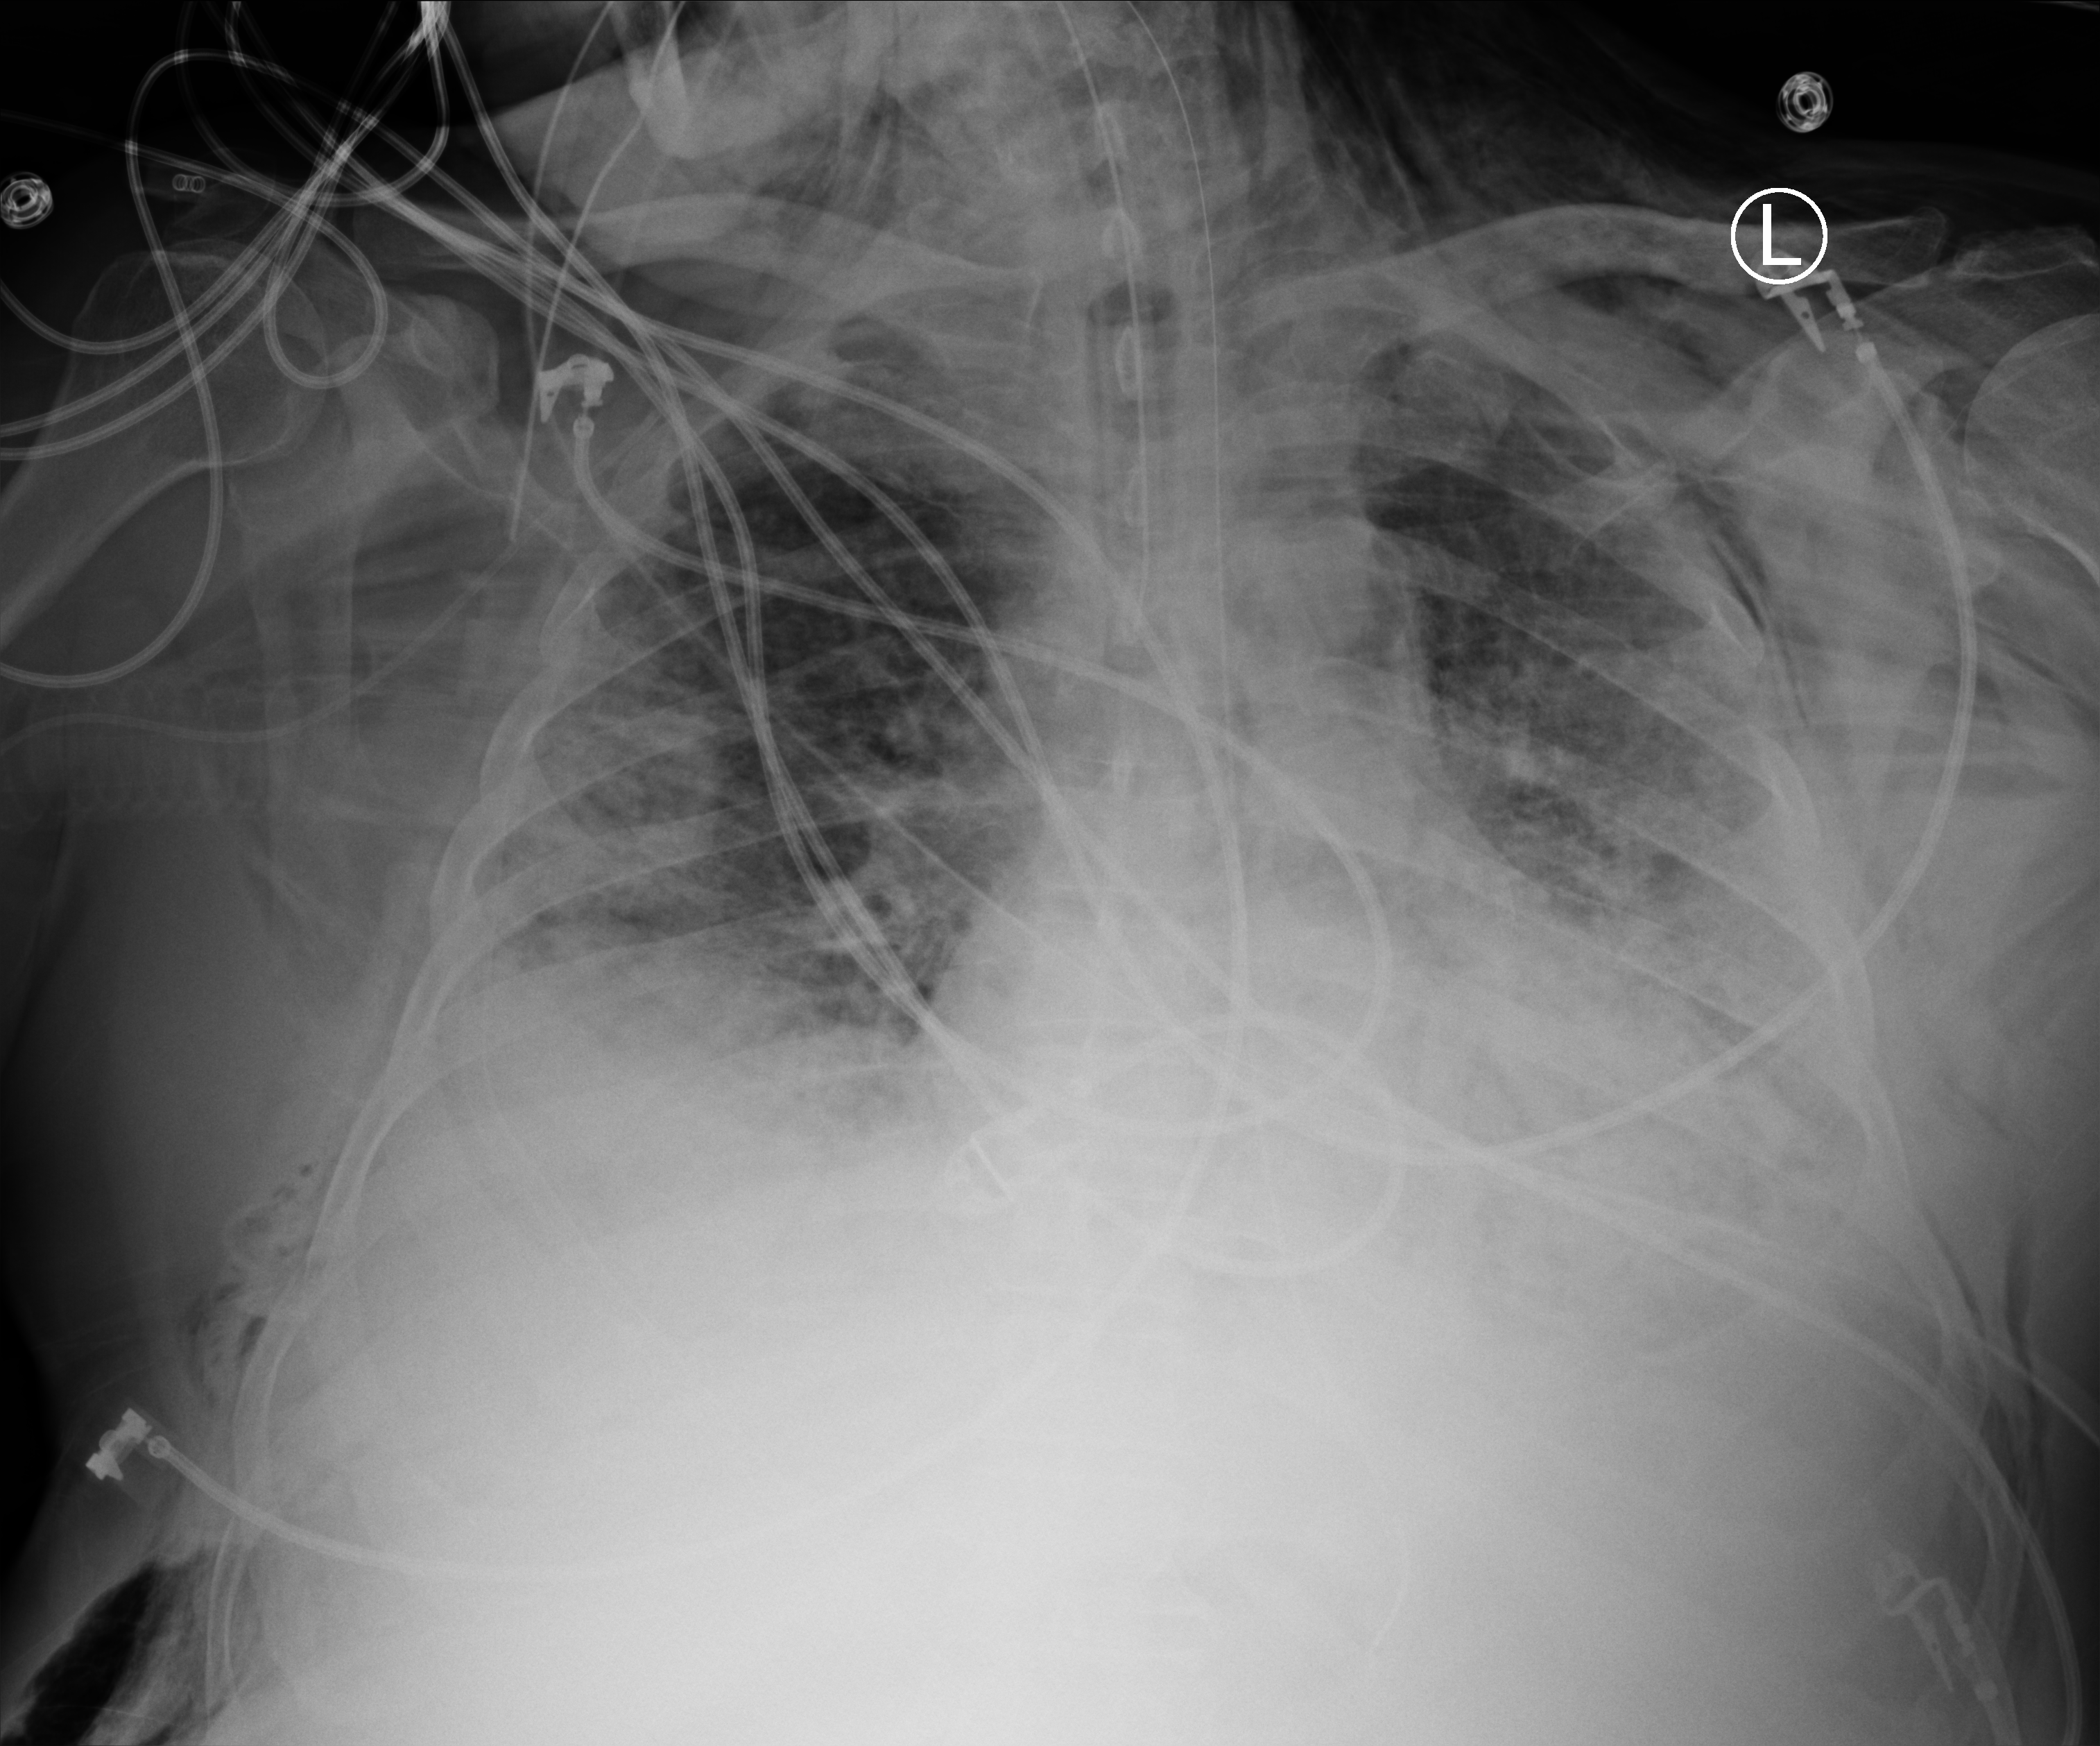
Chest X-ray (portable); anteroposterior (AP) projection. Patient hospitalised with COVID-19; male, aged 60–74 years.
Admission-level facts for this patient (not findings on this image; timing relative to this image not recorded):
- mechanically ventilated during this hospital stay: yes
- other chronic lung disease (admission record): no